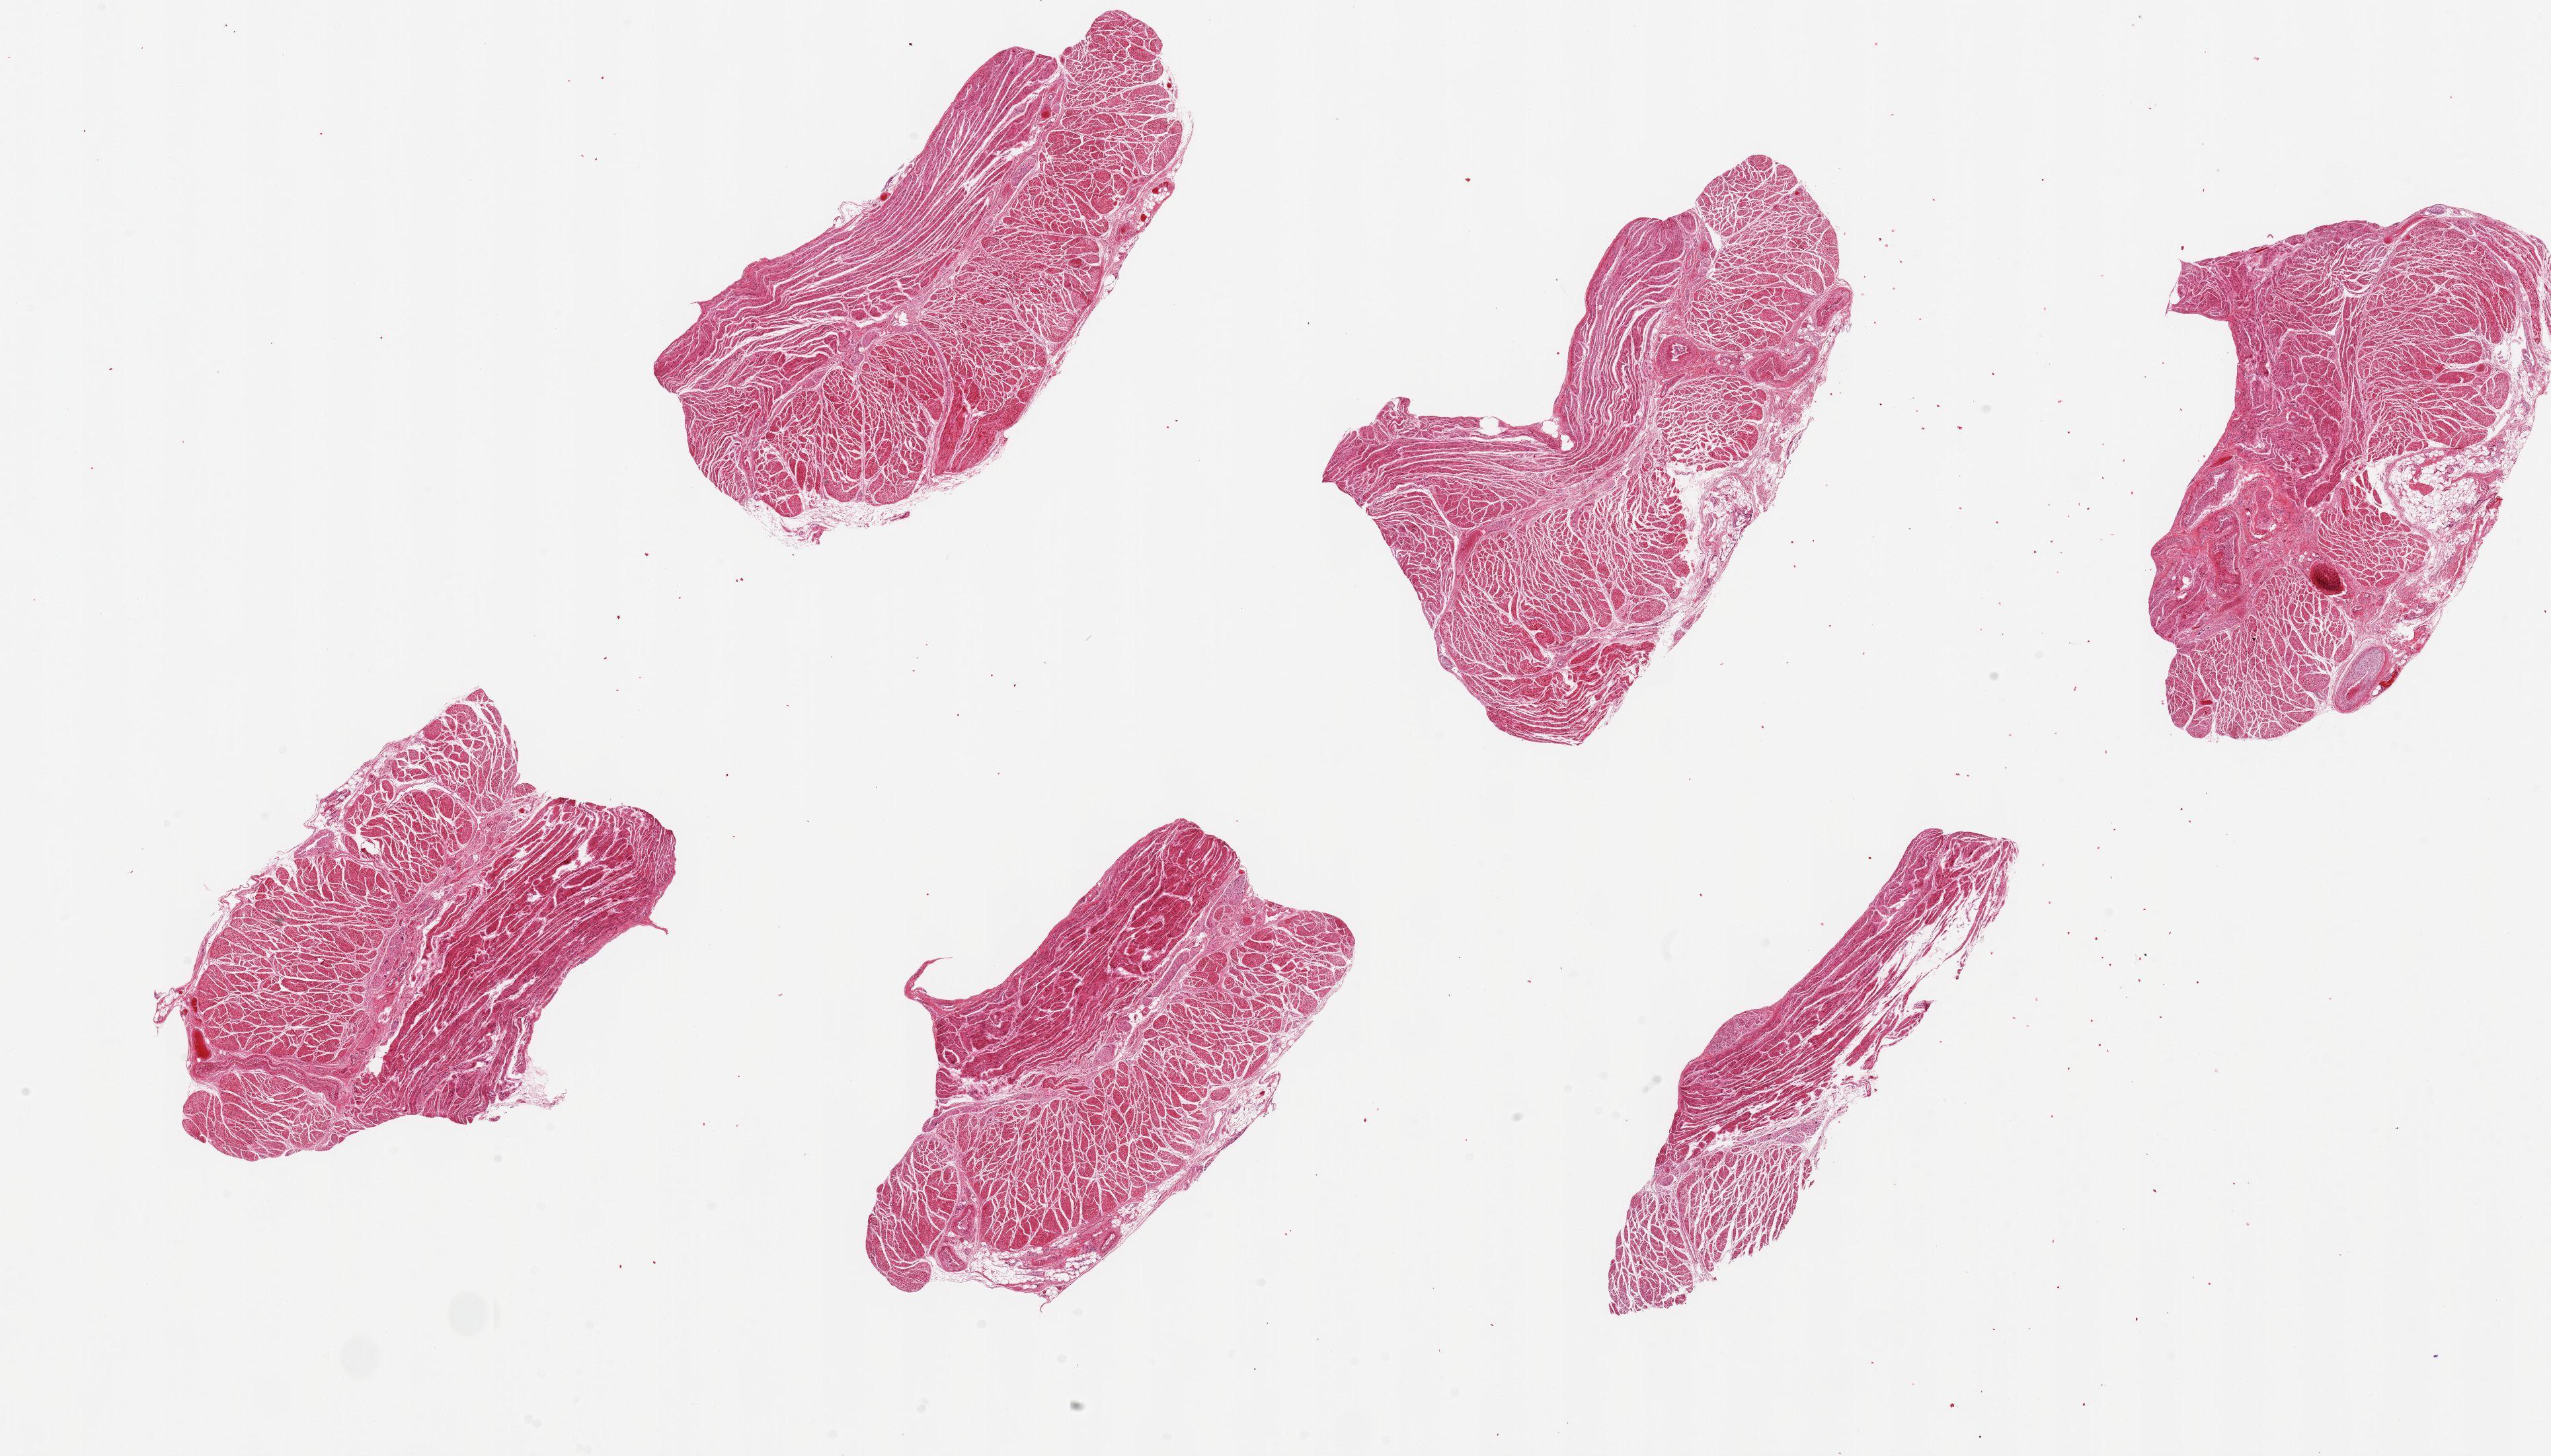
Whole-slide image, H&E stain — whole scanned area (about 30.5 x 17.4 mm) shown as a low-resolution overview, PAXgene-fixed, paraffin-embedded tissue, sampled site (target tissue): gastroesophageal junction, donor tissue sample. Donor sex: male.
Review note (as recorded): 6 pieces, up to 7x4mm; all muscularis, good specimens.